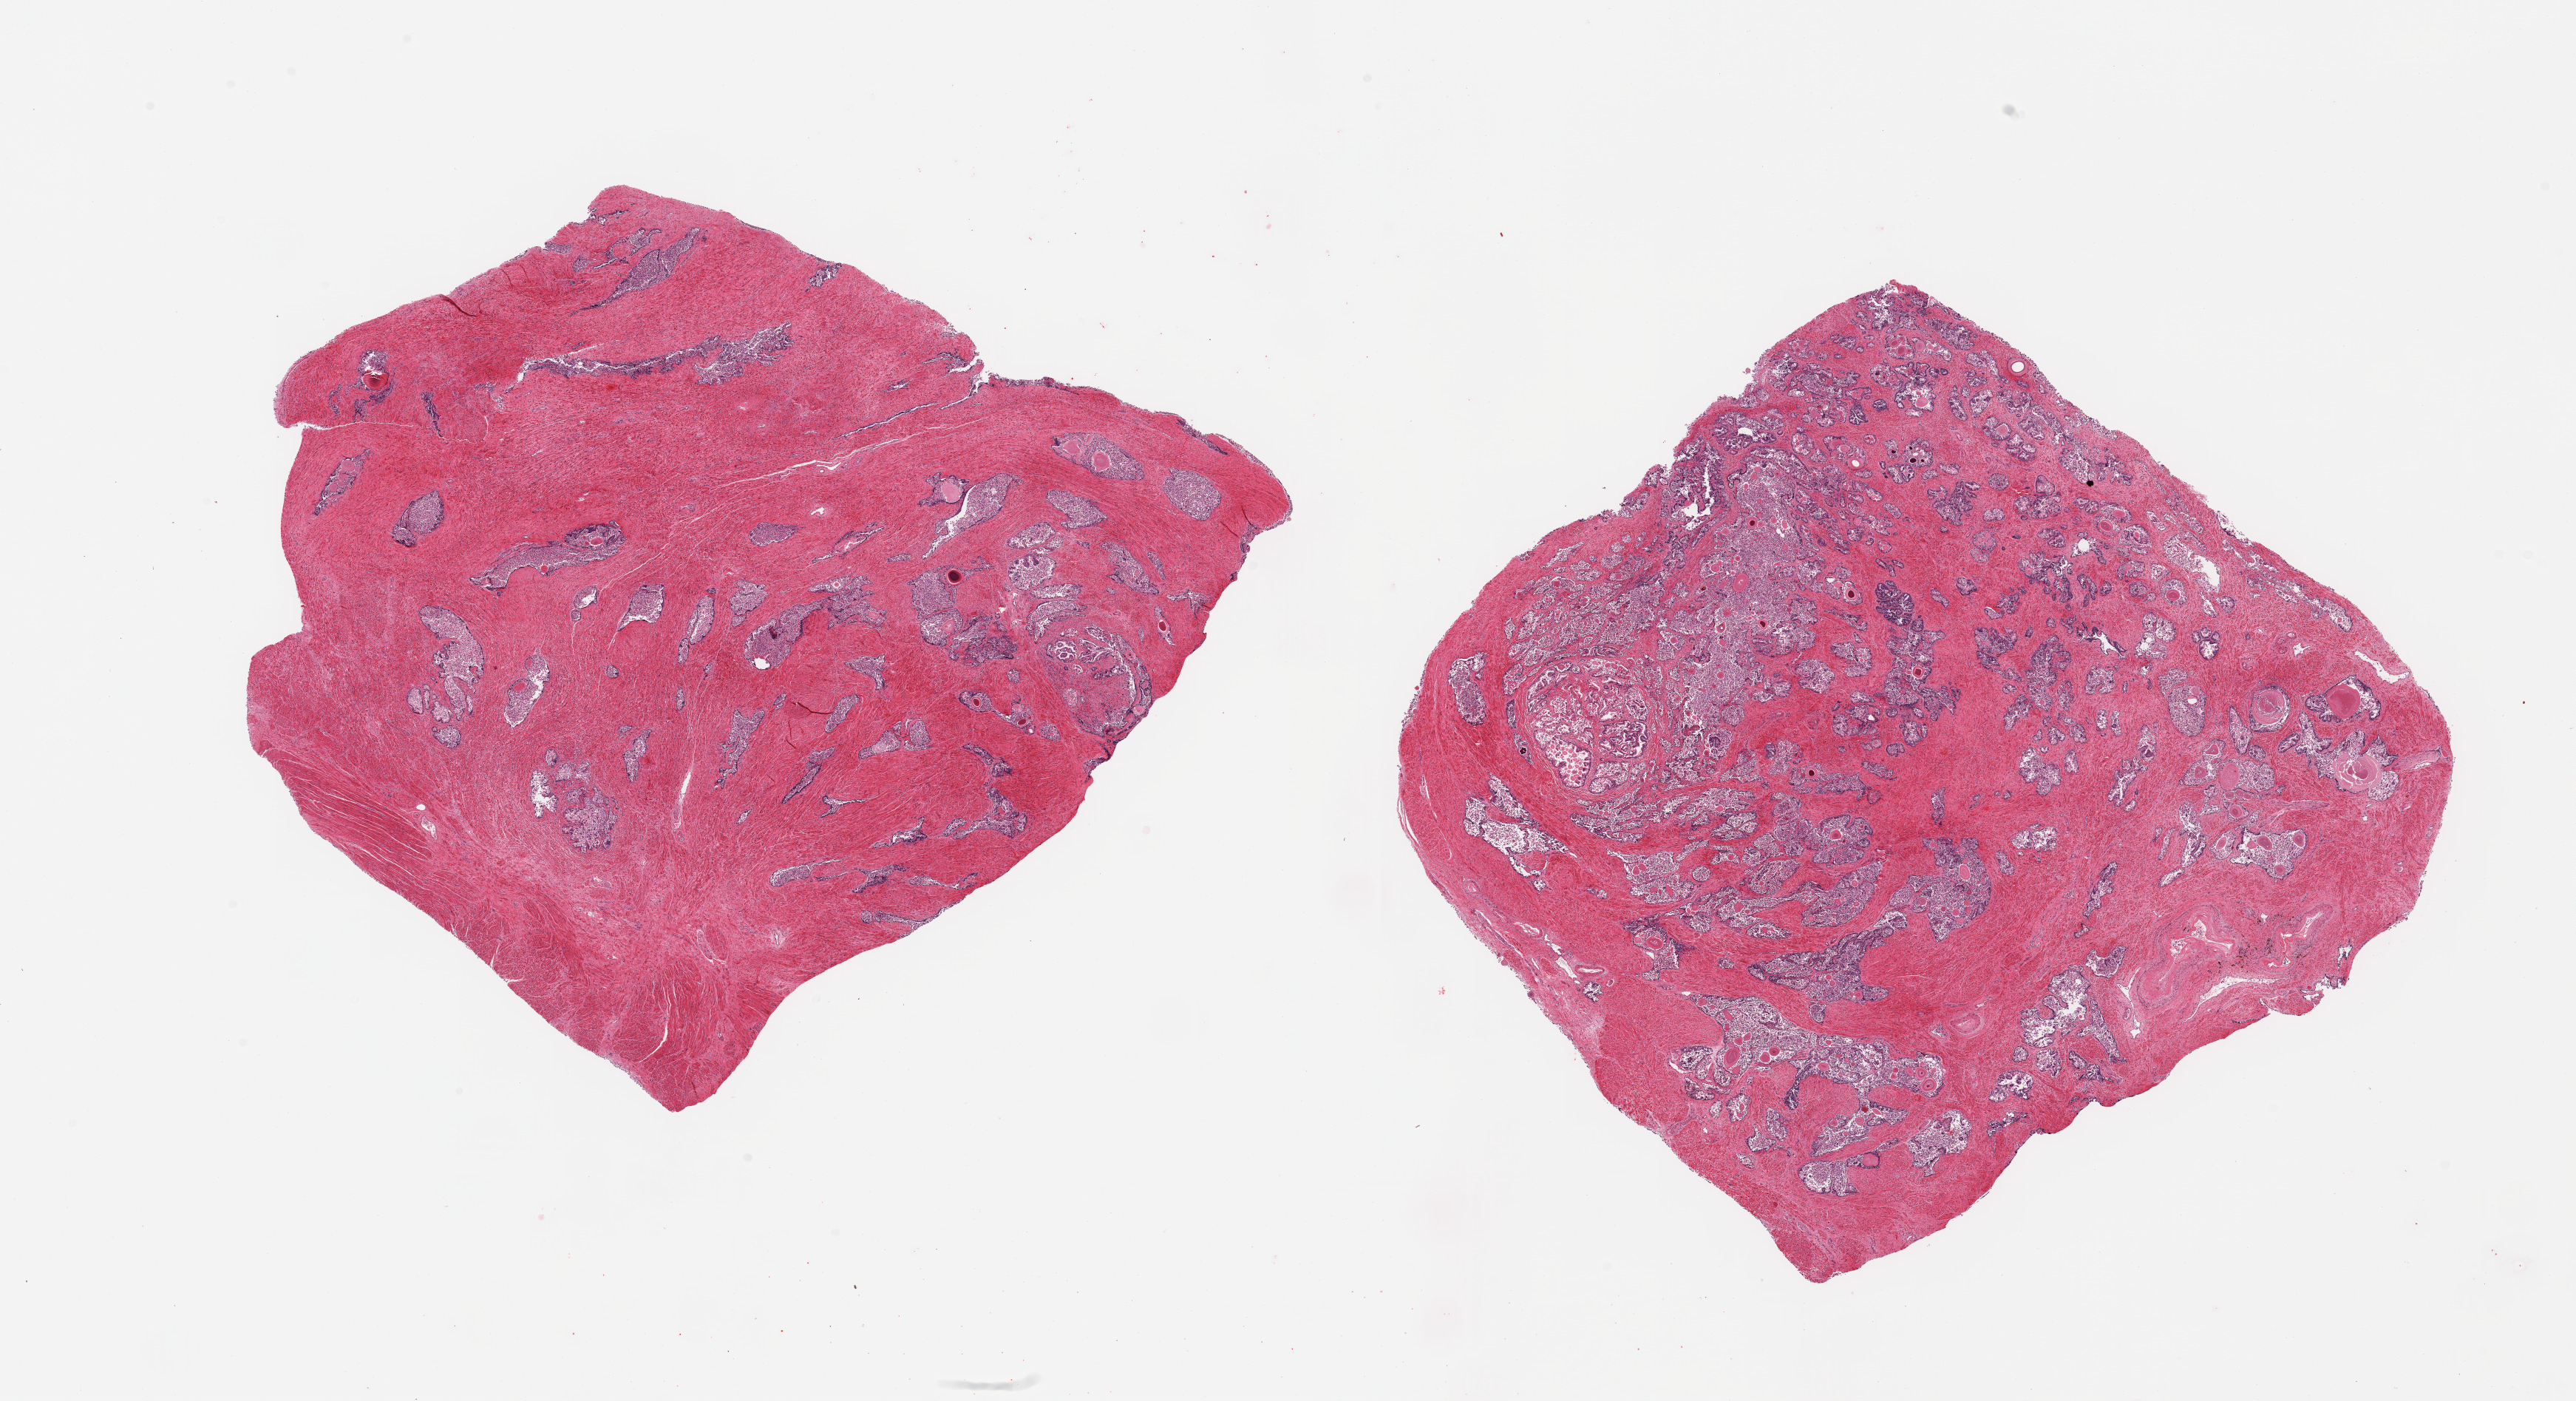
Digitized H&E-stained section, whole scanned area (about 27.6 x 15.0 mm, from a 20x scan) shown as a low-resolution overview; PAXgene-fixed paraffin-embedded (PFPE) section; sampled site (target tissue): prostate; tissue donor sample. Donor: male.
* reviewer comment on this tissue sample: 2 pieces, hyperplastic glandular pattern, glandular elements with moderate-advanced autolysis